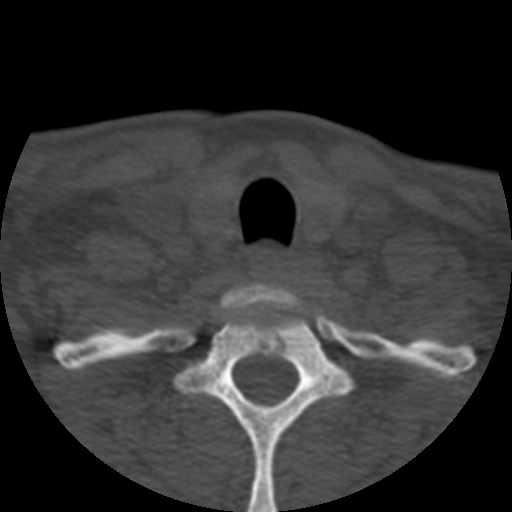
CT including the spine, one axial slice; reconstruction kernel STANDARD; bone window (W 1800 / L 400 HU); 1.25 mm slice thickness; 512 × 512 image matrix. Patient age 57 years. From the clinical record (not read from this slice): primary cancer: prostate.
Structures marked on this image (semi-automatically segmented with operator editing):
- T1 vertebra: box from (x=175, y=284) to (x=352, y=512) px